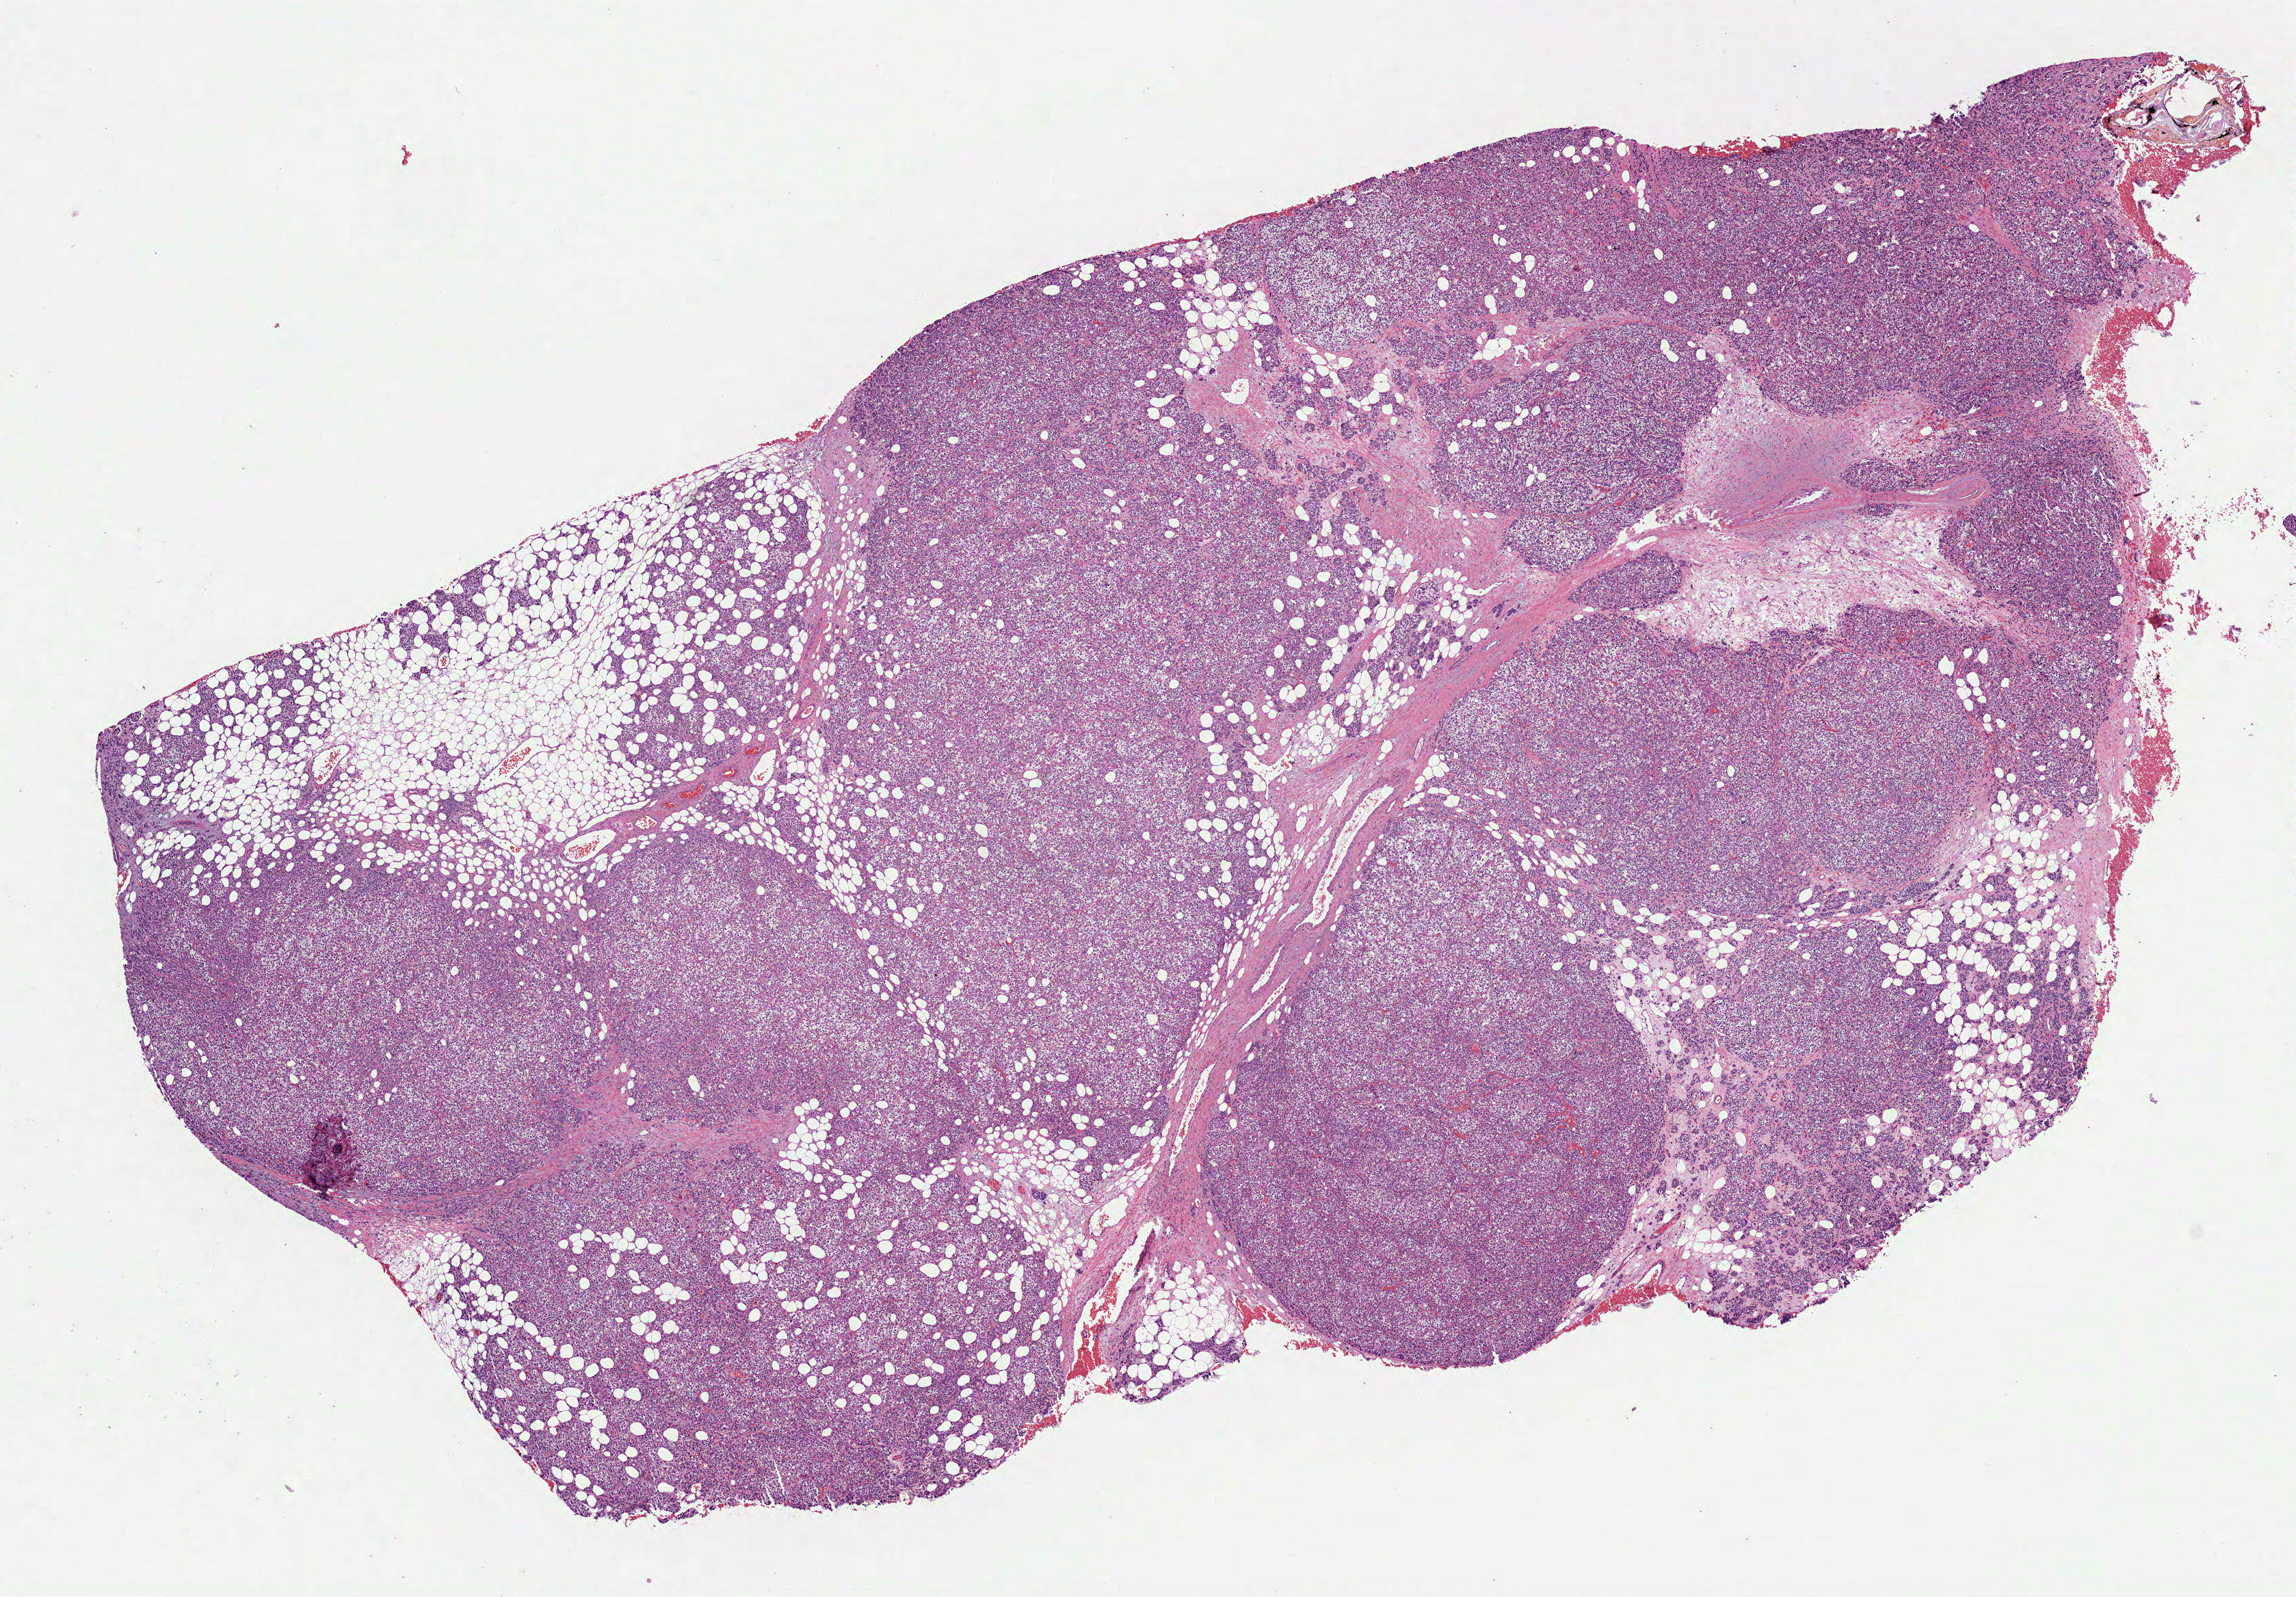
Digitized Hematoxylin and eosin (H&E) stained tissue section (whole slide), low-resolution overview of the scanned area, about 13.5 x 9.4 mm (from a 40x scan); formalin-fixed paraffin-embedded (FFPE) diagnostic section; breast, primary tumour sample. Female, age 87 years at initial diagnosis.
Pathologic diagnosis: Lobular carcinoma, NOS. AJCC pathologic stage: IIB (6th edition).